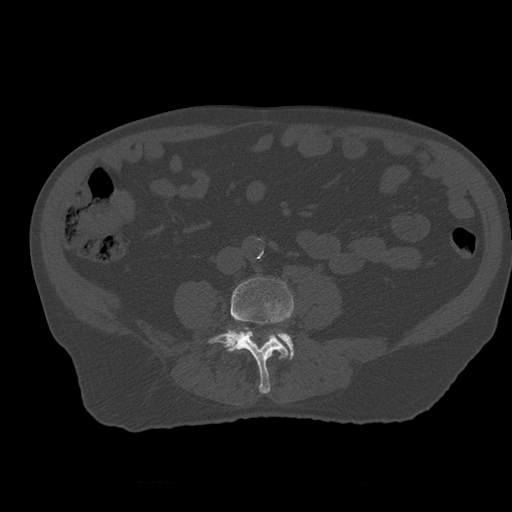
CT including the spine, one axial slice. Slice 161 of 399 in the series (ordered by position). Reconstruction kernel STANDARD. Bone window (W 1800 / L 400 HU). 1.25 mm slice thickness. 512 × 512 image matrix, field of view 407 × 407 mm. Patient age 73 years. Case-level facts recorded for this patient, not image findings: primary cancer: prostate; vertebrae with lytic lesions (as recorded): L2.
Structures marked on this image (semi-automatic segmentation, software-assisted and operator-edited):
- L3 vertebra: bounding box [x1, y1, x2, y2] px = [270, 353, 273, 358]
- L4 vertebra: [208, 278, 294, 394]
- L5 vertebra: [247, 328, 295, 359]